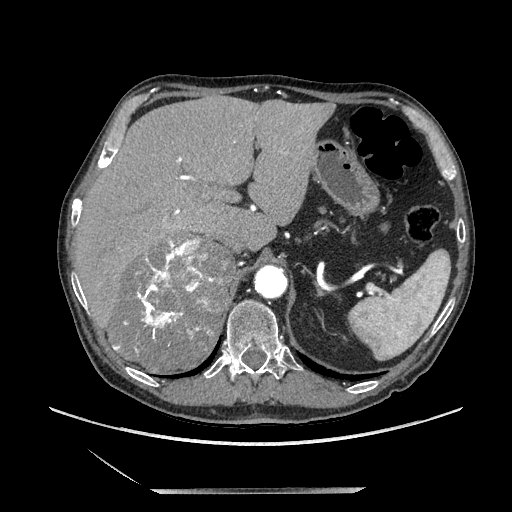
Contrast-enhanced abdominal CT, one axial slice; slice 152 of 243 in the series (ordered by position); soft-tissue window (W 400 / L 40 HU); 512 × 512 image matrix, field of view 420 × 420 mm. Male patient. From the clinical record (not read from this slice): diagnosis: adrenocortical carcinoma; tumour side: right adrenal; tumour size at pathology: 16 cm; Ki-67 index: 17 %; stage (as recorded): 3.
Annotated regions visible in this slice (semi-automatic segmentation, software-assisted and operator-edited):
- mass: box from (x=110, y=233) to (x=232, y=373) px